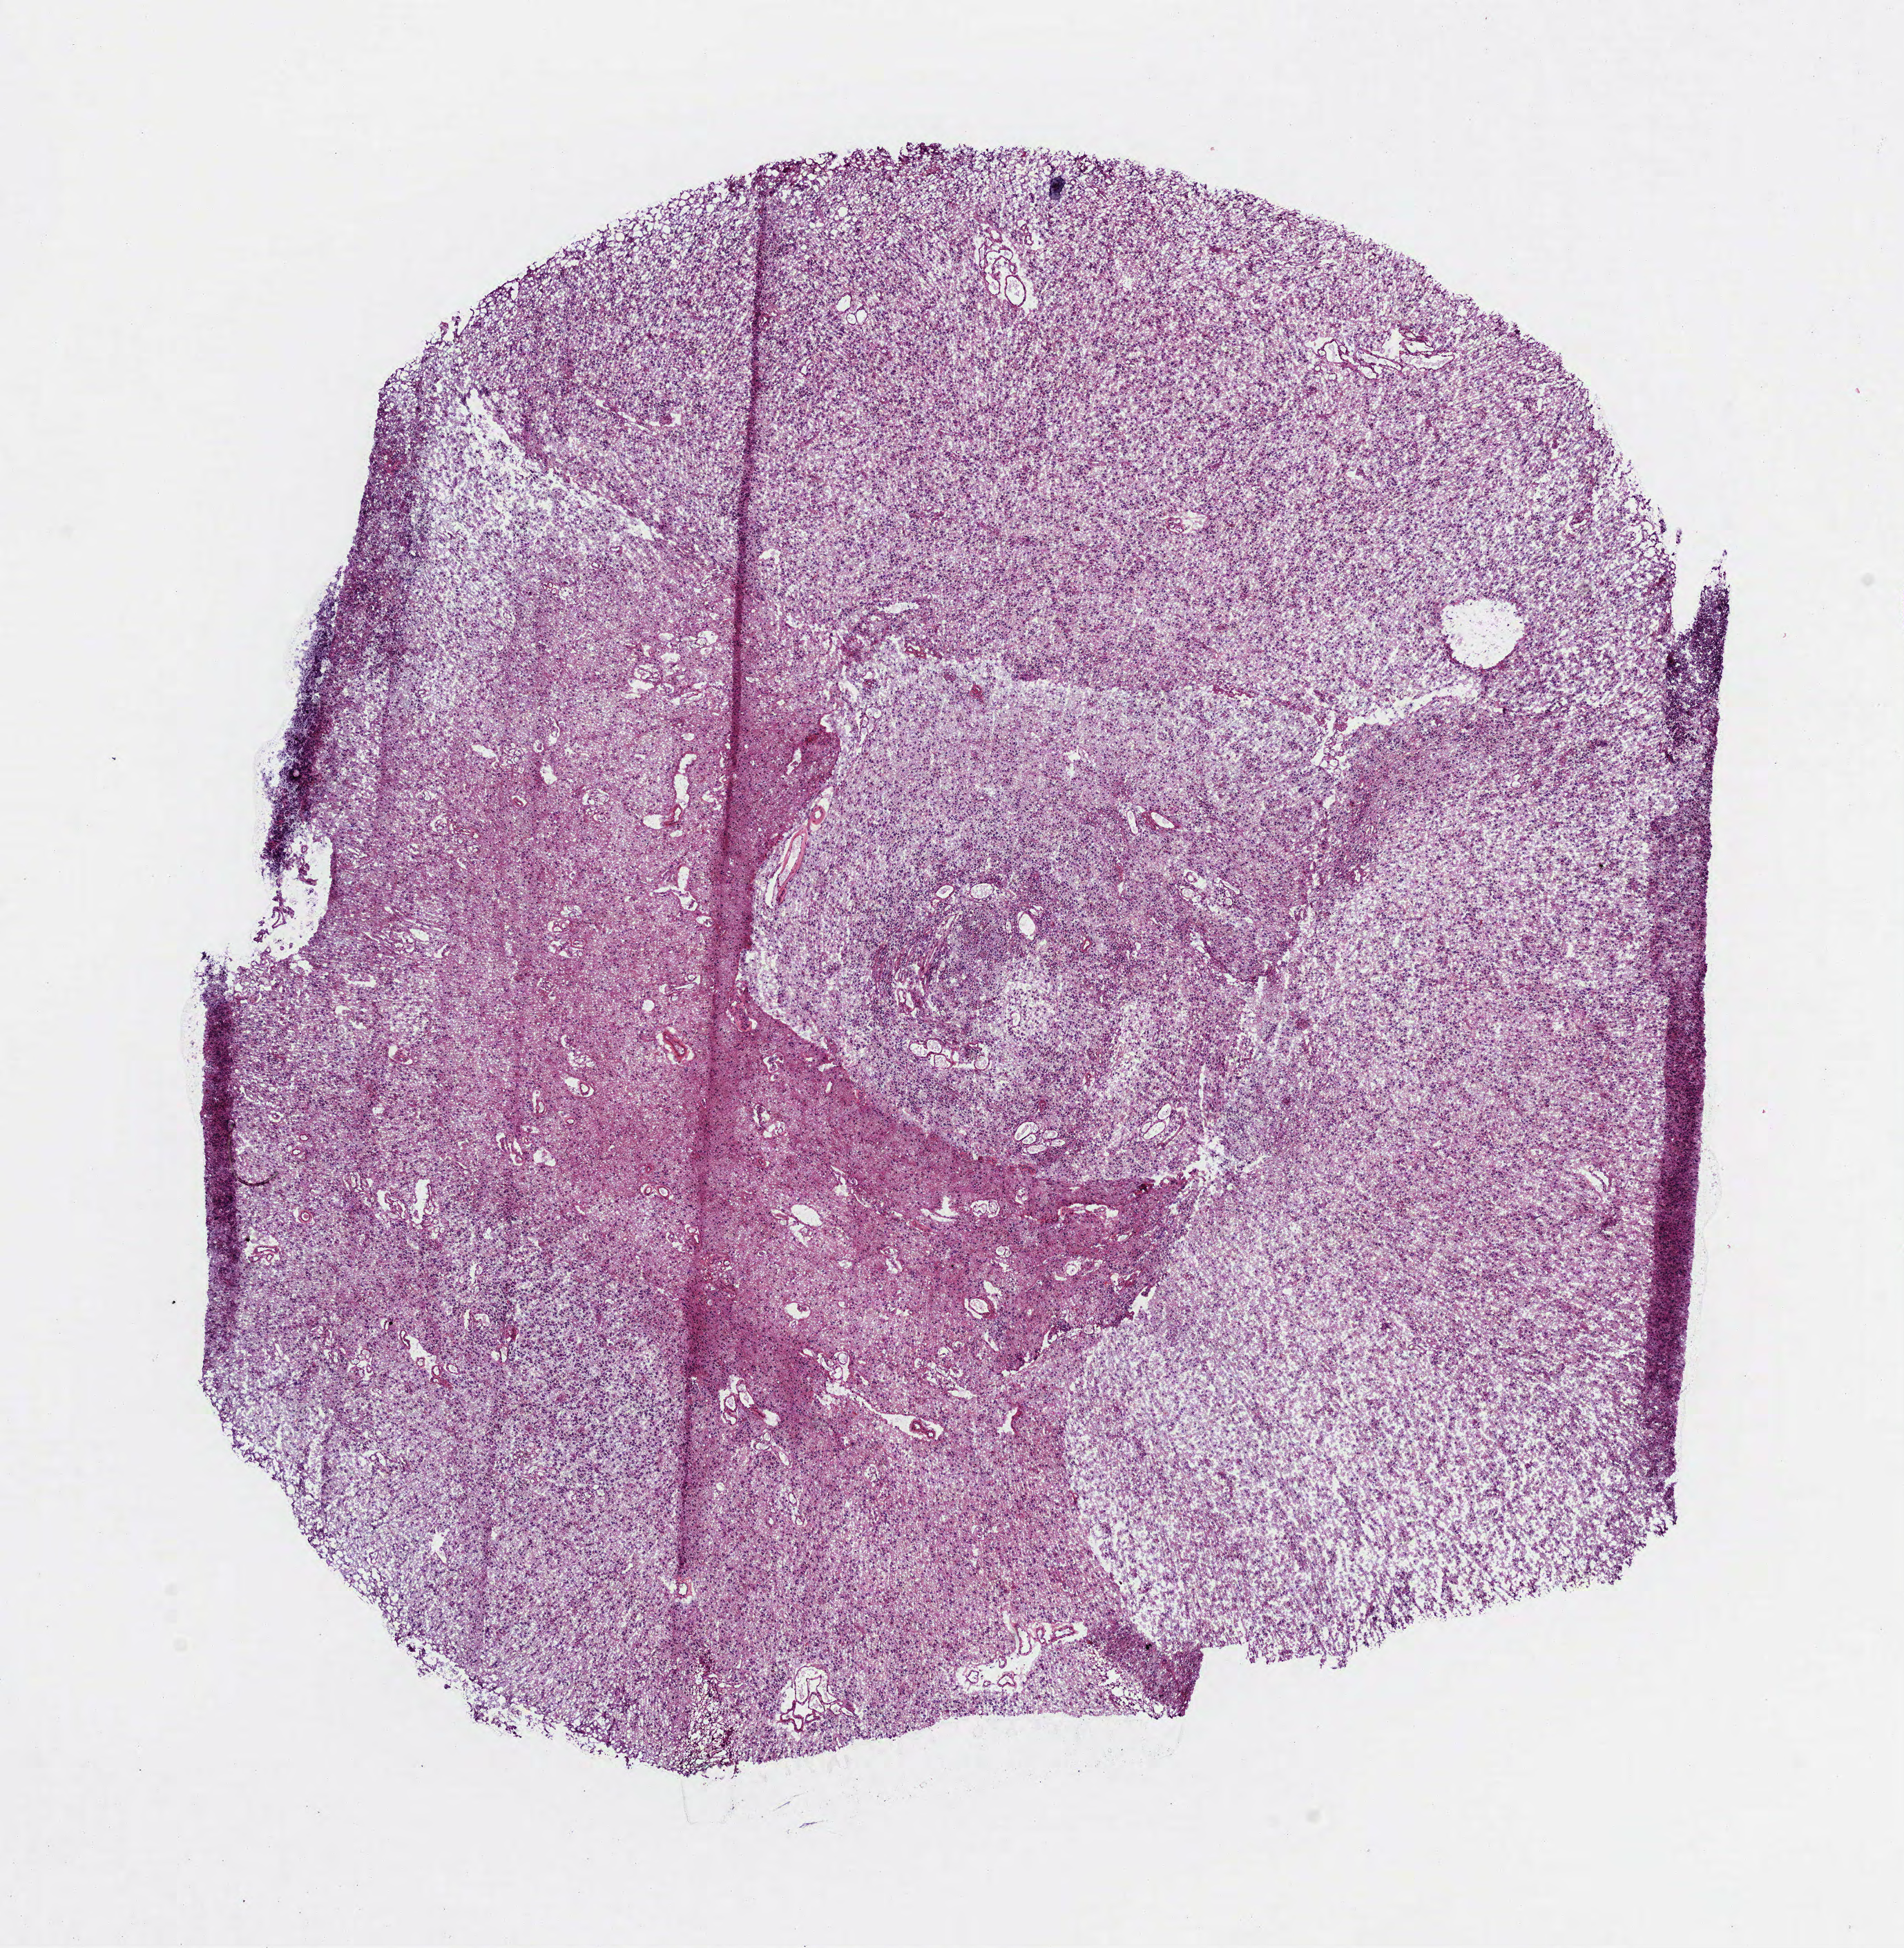
Digitized H&E tissue section (whole slide) — low-resolution overview of the scanned area, about 11.1 x 11.4 mm (from a 40x scan). Frozen section from the bottom of the tissue portion. Sample: primary tumour, brain. Male patient; age at initial diagnosis 59 years. Histologic grade: G2 (moderately differentiated). Composition of this section per pathologist review: tumour cells 100%, tumour nuclei 80%, normal cells 0%, stromal cells 0%, necrosis 0%.
Laterality: right. Diagnosis: Oligodendroglioma, NOS (cerebrum).